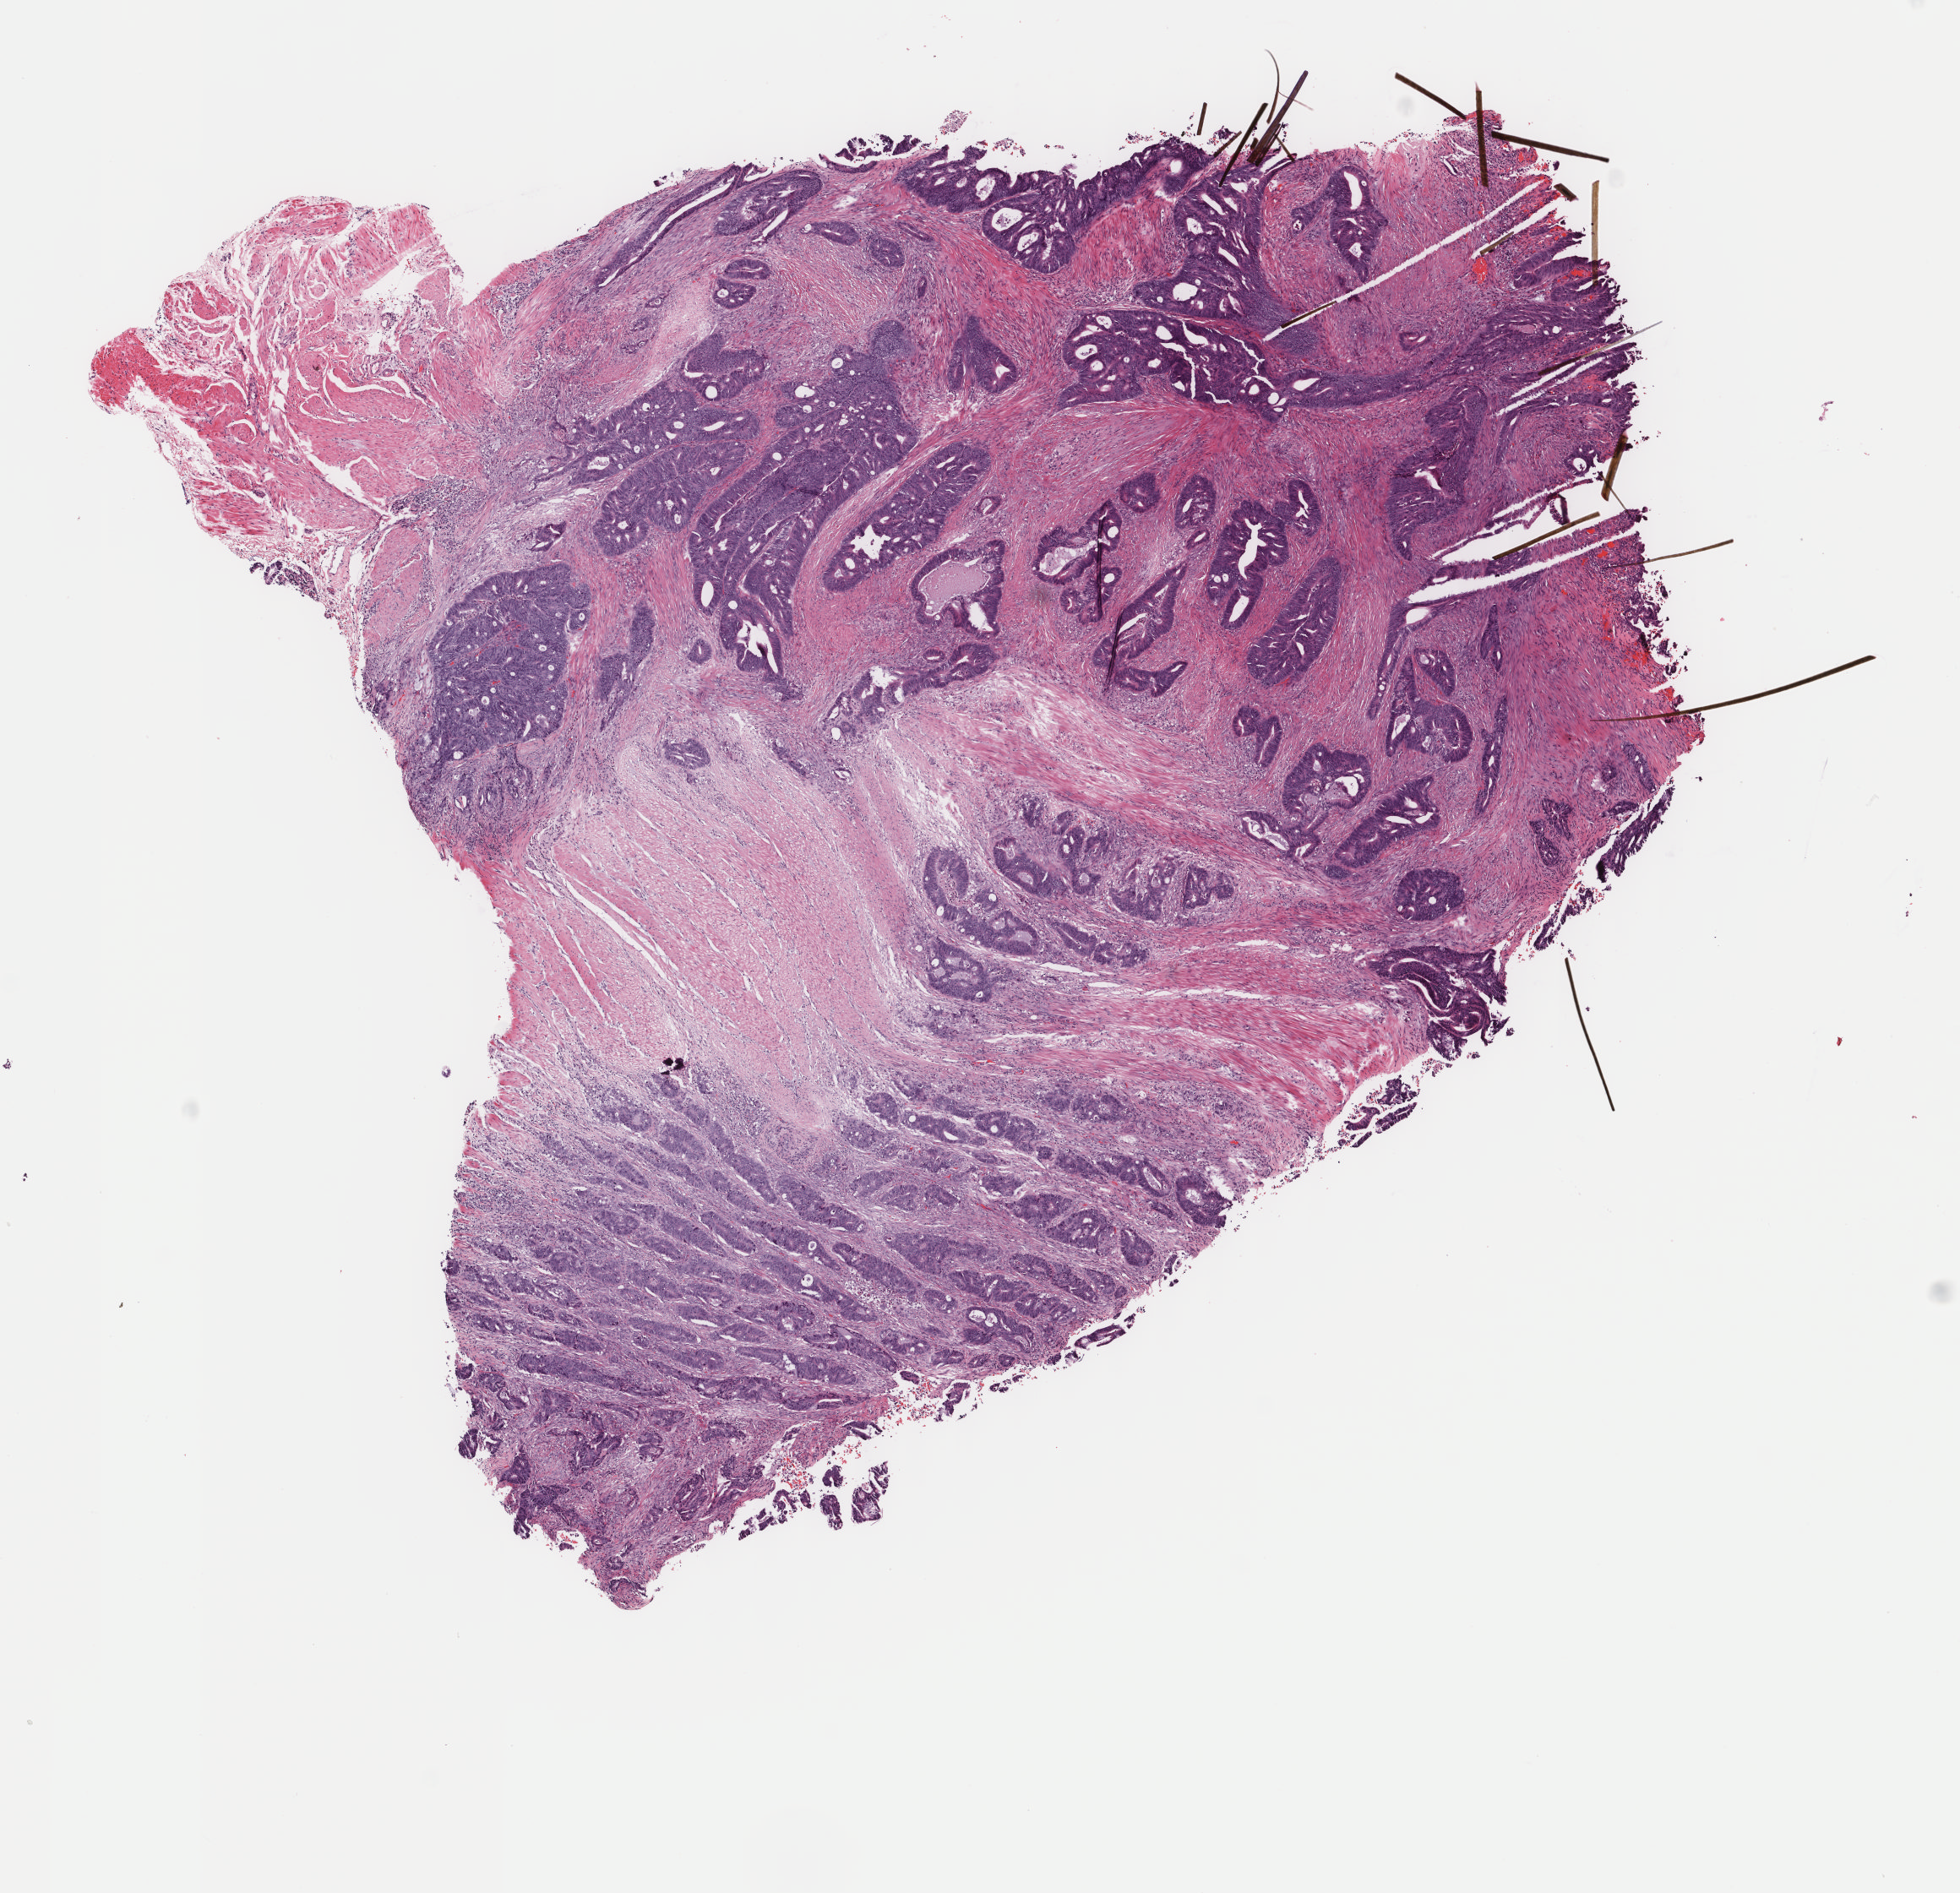
H&E whole-slide image, whole scanned area (about 9.2 x 8.9 mm, from a 40x scan) shown as a low-resolution overview, frozen section, primary tumour sample from the colon. Female, age 75 years at initial diagnosis. Pathologist review of this section (percent, as recorded): tumour cells 80%, tumour nuclei 80%.
Pathologic diagnosis: Adenocarcinoma, NOS.